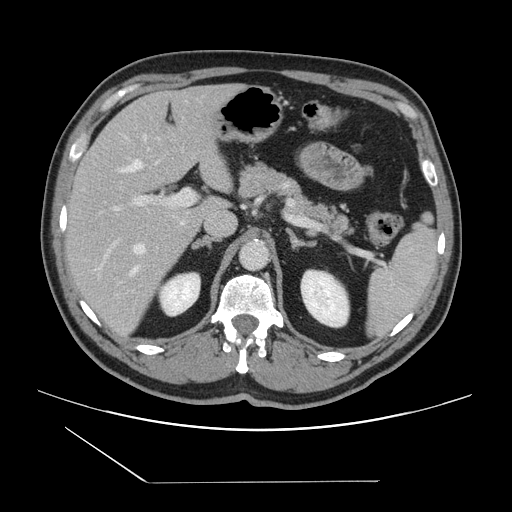
Contrast-enhanced abdominal CT, one axial slice; position 88 of 157 along the scan axis; intravenous contrast given; soft-tissue window (W 400 / L 40 HU); 2.5 mm slice thickness; 512 × 512 image matrix. Male patient, age 61 years. Case-level facts recorded for this patient, not image findings: diagnosis: colorectal cancer liver metastases, imaged before liver resection.
Outlined on this slice (expert manual segmentation):
- hepatic veins: bounding box (x1, y1, x2, y2) in pixels: (100, 137, 146, 272)
- liver: (66, 85, 239, 338)
- planned liver remnant (the part of the liver to remain after resection): (67, 85, 233, 221)
- portal vein (with intrahepatic branches): (104, 188, 195, 260)